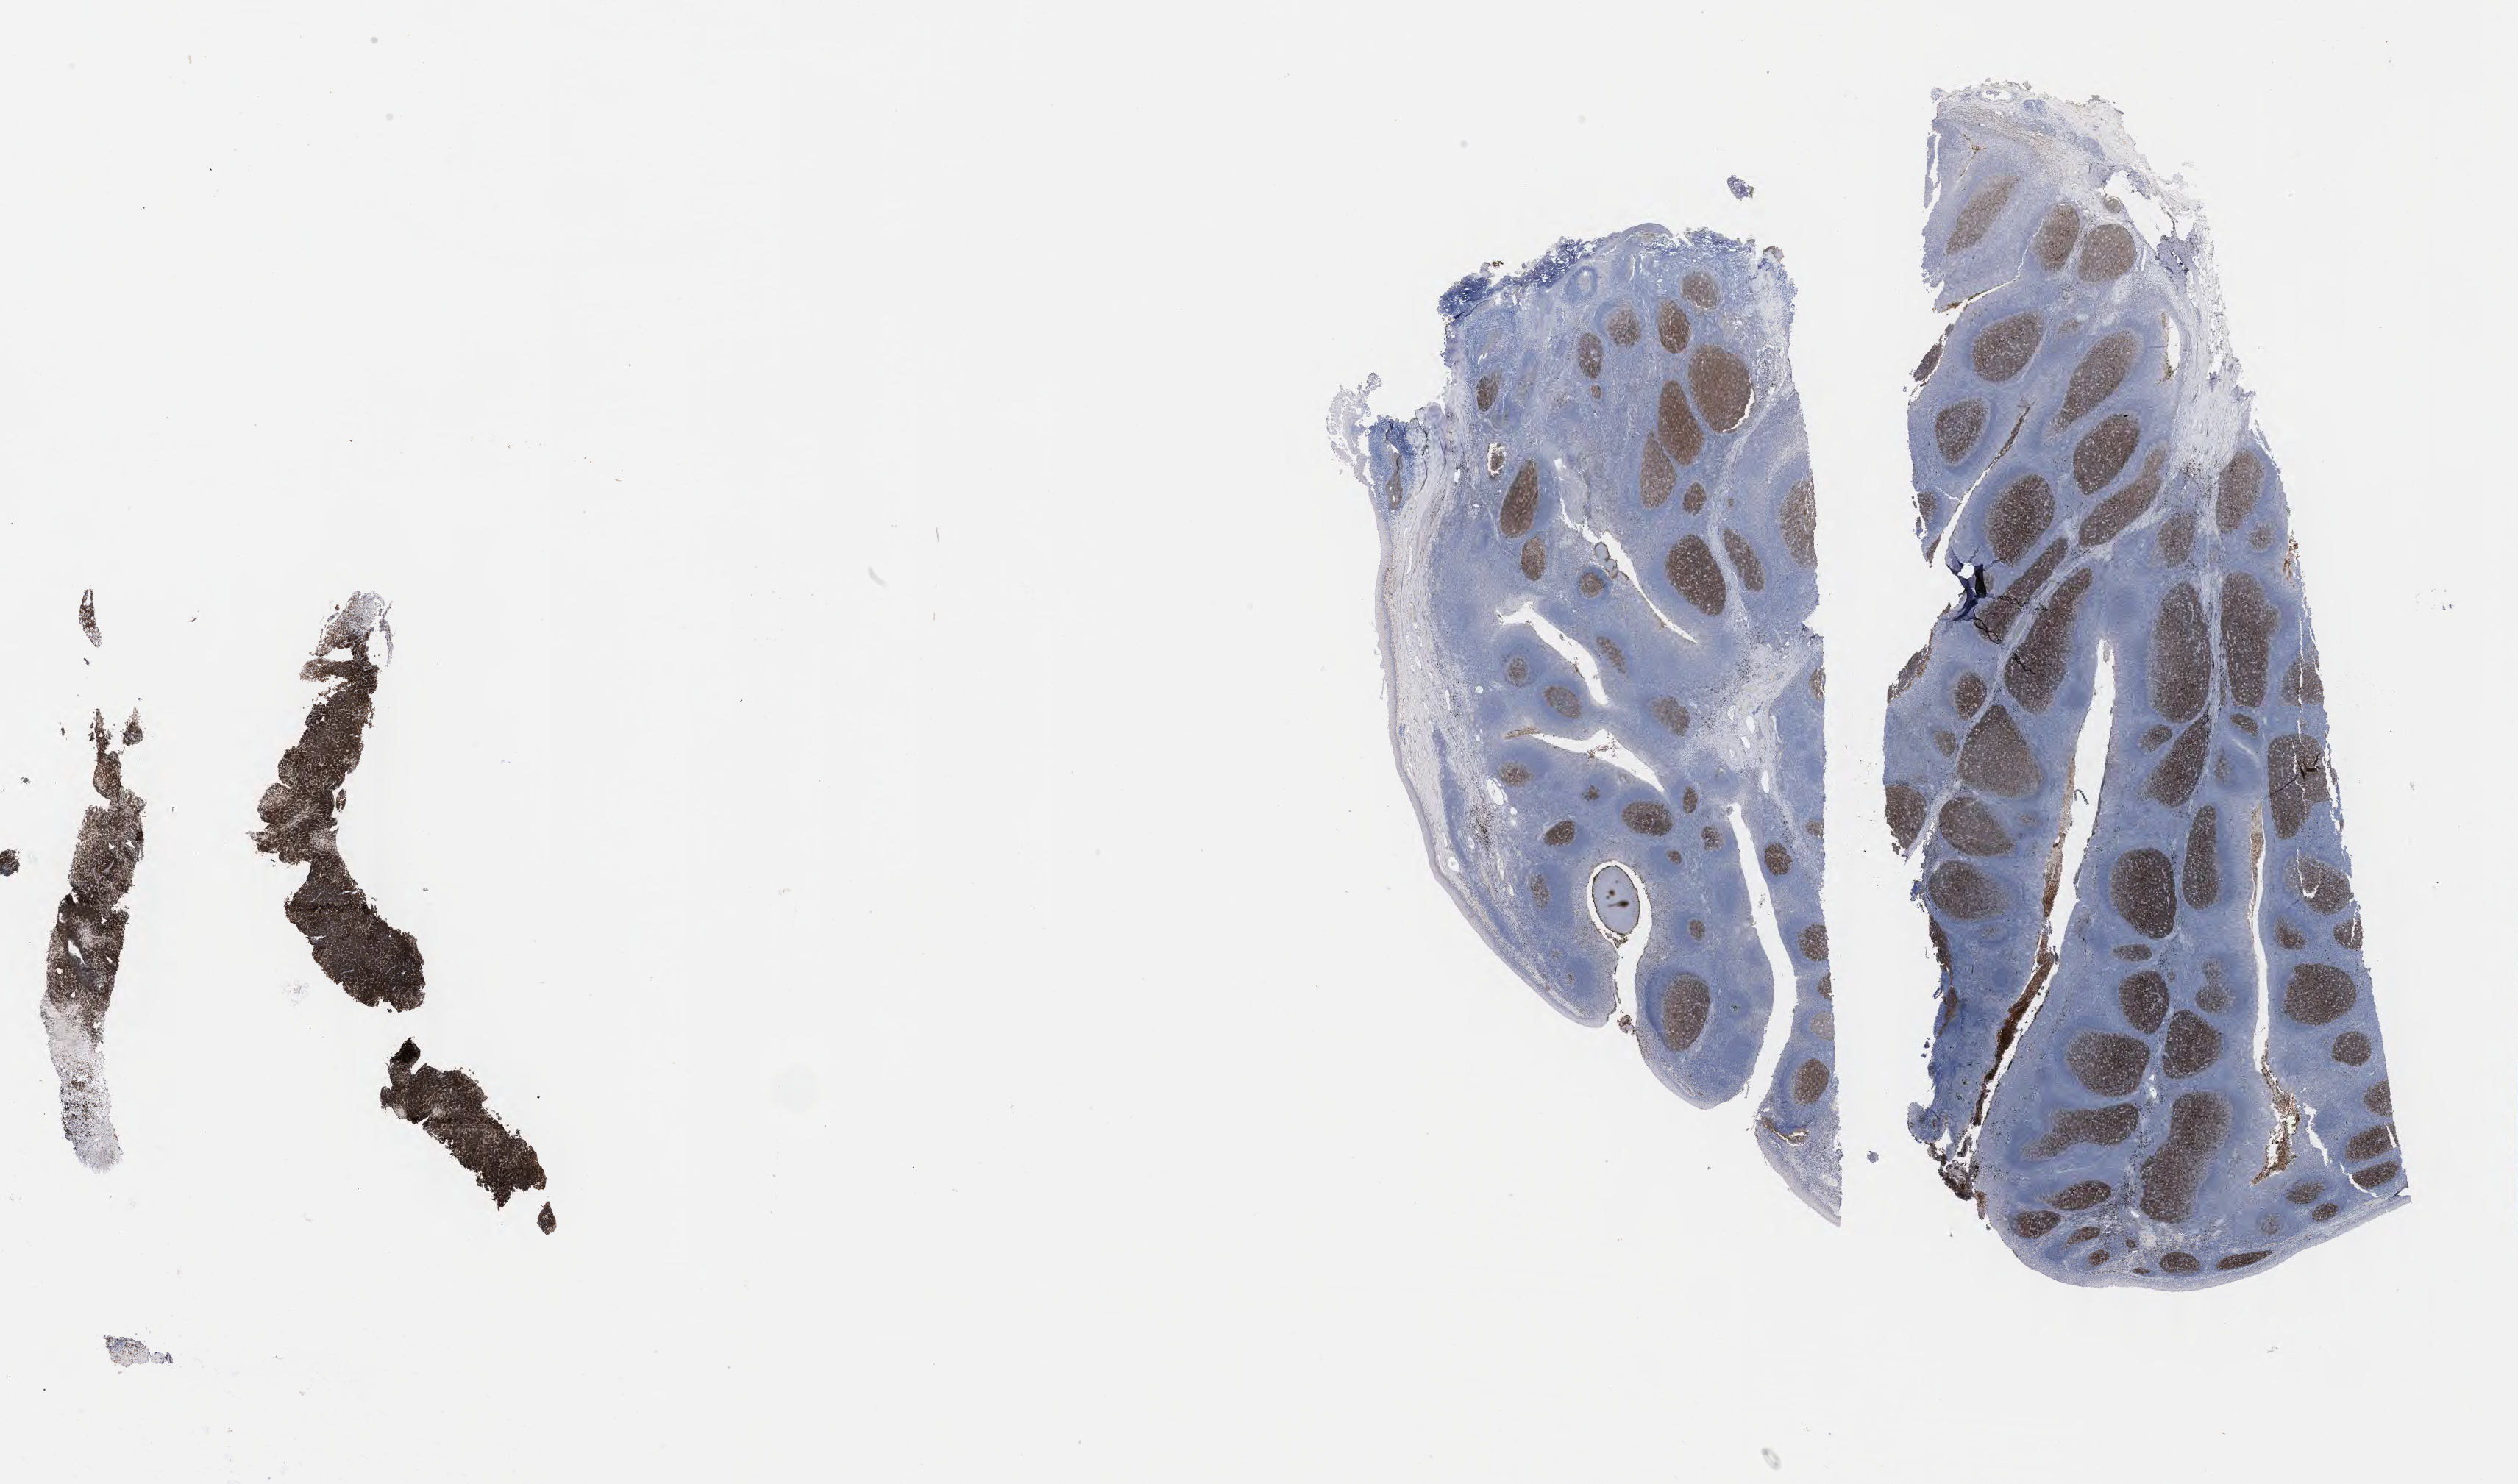
Whole-slide image, immunohistochemical stain for CD10, shown as a low-resolution overview of the whole scanned area (about 27.7 x 16.3 mm). Specimen: tumor tissue. Female patient, age 12 years.
Diagnosis: Burkitt lymphoma, NOS.